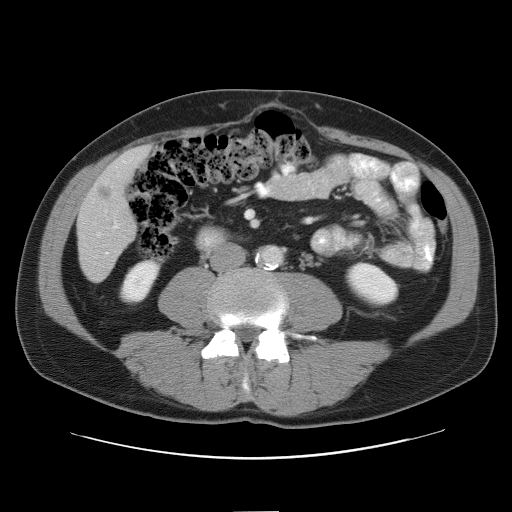
Contrast-enhanced abdominal CT, one axial slice. Position 16 of 52 along the scan axis. Reconstruction kernel STANDARD. 120 kVp. Intravenous contrast given. Soft-tissue window (W 400 / L 40 HU). 5 mm slice thickness. 512 × 512 image matrix, field of view 393 × 393 mm. Male patient, age 70 years. Case-level facts recorded for this patient, not image findings: diagnosis: colorectal cancer liver metastases, imaged before liver resection; multiple liver metastases: yes.
Annotated regions visible in this slice (manually delineated by an expert):
- liver: bounding box (x1, y1, x2, y2) in pixels: (78, 147, 148, 281)
- planned liver remnant (the part of the liver to remain after resection): (121, 147, 149, 171)
- portal vein (with intrahepatic branches): (114, 223, 119, 229)
- liver metastasis: (98, 188, 112, 201)